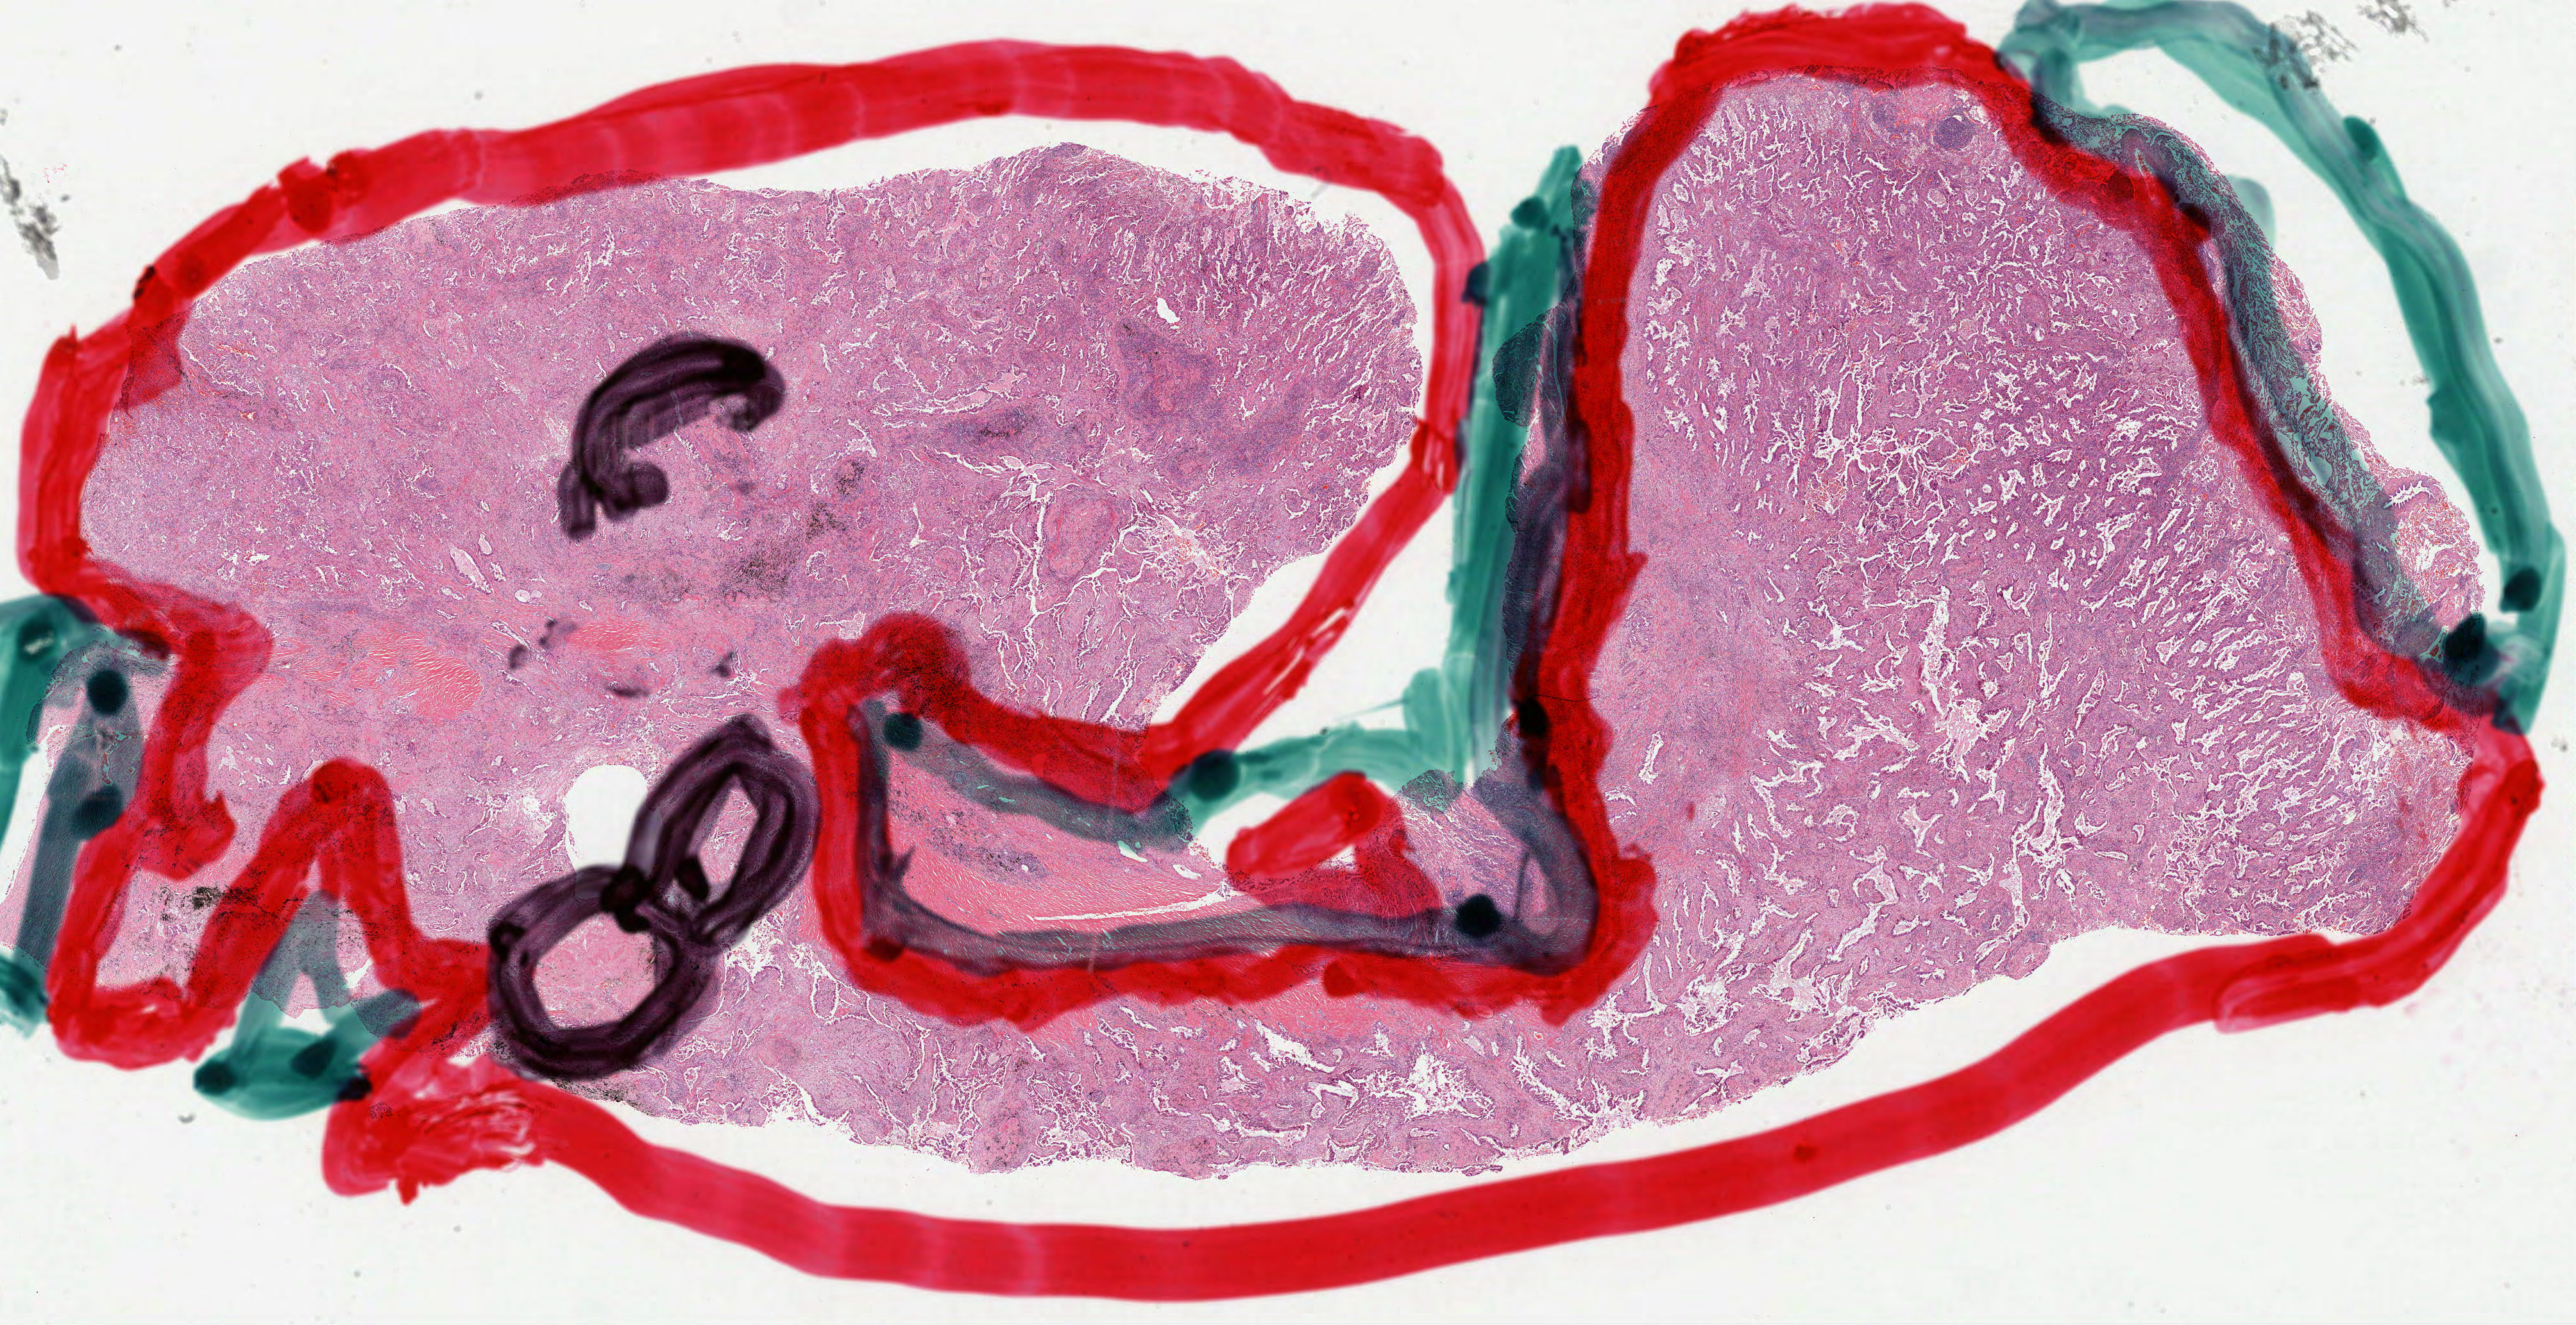
Digitized H&E tissue section (whole slide) — whole scanned area (about 32.4 x 16.7 mm, slide scanned at 40x) shown as a low-resolution overview. Formalin-fixed paraffin-embedded (FFPE) diagnostic section. Primary tumour sample from the lung. Patient: male, age at initial diagnosis 79 years.
AJCC pathologic stage: IIA. Diagnosis: Adenocarcinoma, NOS (upper lobe, lung).